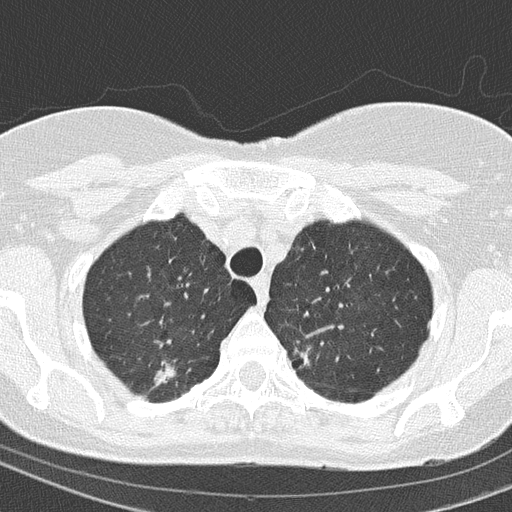
Chest CT (low-dose screening protocol), one axial image, first (baseline) screen, lung window (W 1500 / L -600 HU), 2 mm slice thickness, slice 27 of 154 in the series. Female participant, aged 67 years at enrolment. Current smoker at enrolment.
- Lesion marked by an expert reader, bounding box (x1, y1, x2, y2) in pixels: (136, 349, 195, 401).
- The exam's reader record, not a measurement of the box and not confirmed to be the same lesion: non-calcified nodule or mass ≥4 mm, right upper lobe, 15 × 14 mm, spiculated (stellate) margins, soft tissue attenuation.
- Official screen result: positive, change unspecified: nodule(s) >= 4 mm or enlarging nodule(s), mass(es), or other non-specific abnormalities suspicious for lung cancer.
- Lung cancer was diagnosed 63 days after this screen: adenocarcinoma, NOS, right upper lobe, moderately differentiated (G2), stage IA (AJCC 6th edition), 14 mm at pathology.